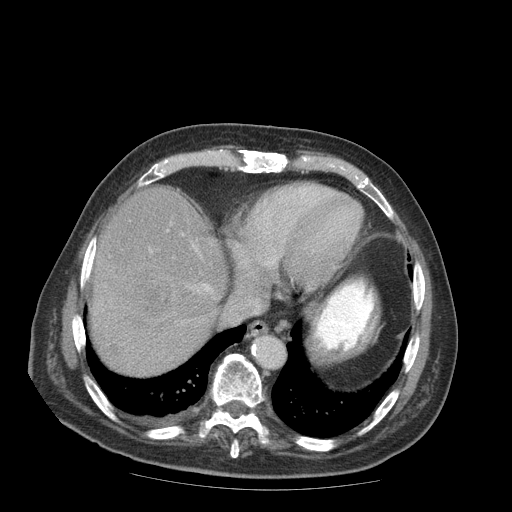
Contrast-enhanced abdominal CT (liver protocol), one axial slice. Position 77 of 99 along the scan axis. Reconstruction kernel STANDARD. 140 kVp. Soft-tissue window (W 400 / L 40 HU). 2.5 mm slice thickness. 512 × 512 image matrix. From the clinical record (not read from this slice): diagnosis: hepatocellular carcinoma (patient treated with transarterial chemoembolisation; whether this scan precedes or follows treatment is not stated here); TNM stage (as recorded): Stage-IIIB; Child-Pugh class: A; tumour nodularity: multinodular.
Structures marked on this image (semi-automatically segmented with operator editing):
- liver parenchyma outside the tumour (the mass and vessels are separate outlines, so this box may not span the whole liver): bounding box <90,186,226,375> (left, top, right, bottom; pixels)
- mass: <92,258,175,345>
- liver vessels: <167,230,213,293>